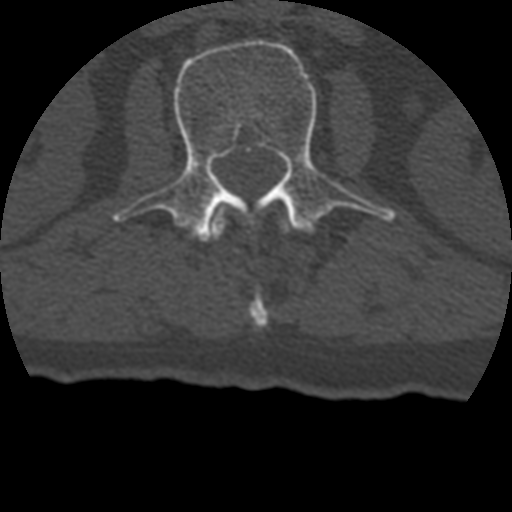
CT including the spine, one axial slice. Position 121 of 399 along the scan axis. Reconstruction kernel STANDARD. 120 kVp. Bone window (W 1800 / L 400 HU). 1.25 mm slice thickness. 512 × 512 image matrix, field of view 160 × 160 mm. Patient age 69 years. Case-level facts recorded for this patient, not image findings: primary cancer: prostate.
Structures marked on this image (semi-automatically segmented with operator editing):
- L1 vertebra: bounding box (x1, y1, x2, y2) in pixels: (210, 201, 291, 327)
- L2 vertebra: (111, 40, 397, 242)